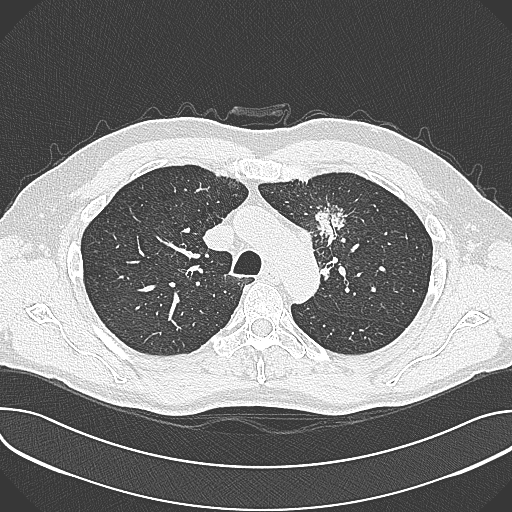
Low-dose screening chest CT, axial slice; baseline screening round; lung window (W 1500 / L -600 HU); slice 93 of 361 in the series. Male participant, aged 59 years at enrolment. Current smoker at enrolment.
Expert reader's lesion annotation, bounding box (x1, y1, x2, y2) in pixels: (302, 199, 359, 257). The screening reader recorded 2 non-calcified nodules or masses ≥4 mm on this exam; which of them this box marks is not recorded. Lung cancer was diagnosed 21 days after this screen: non-small cell carcinoma, left upper lobe, poorly differentiated (G3), stage IIIA (AJCC 6th edition), 35 mm at pathology.